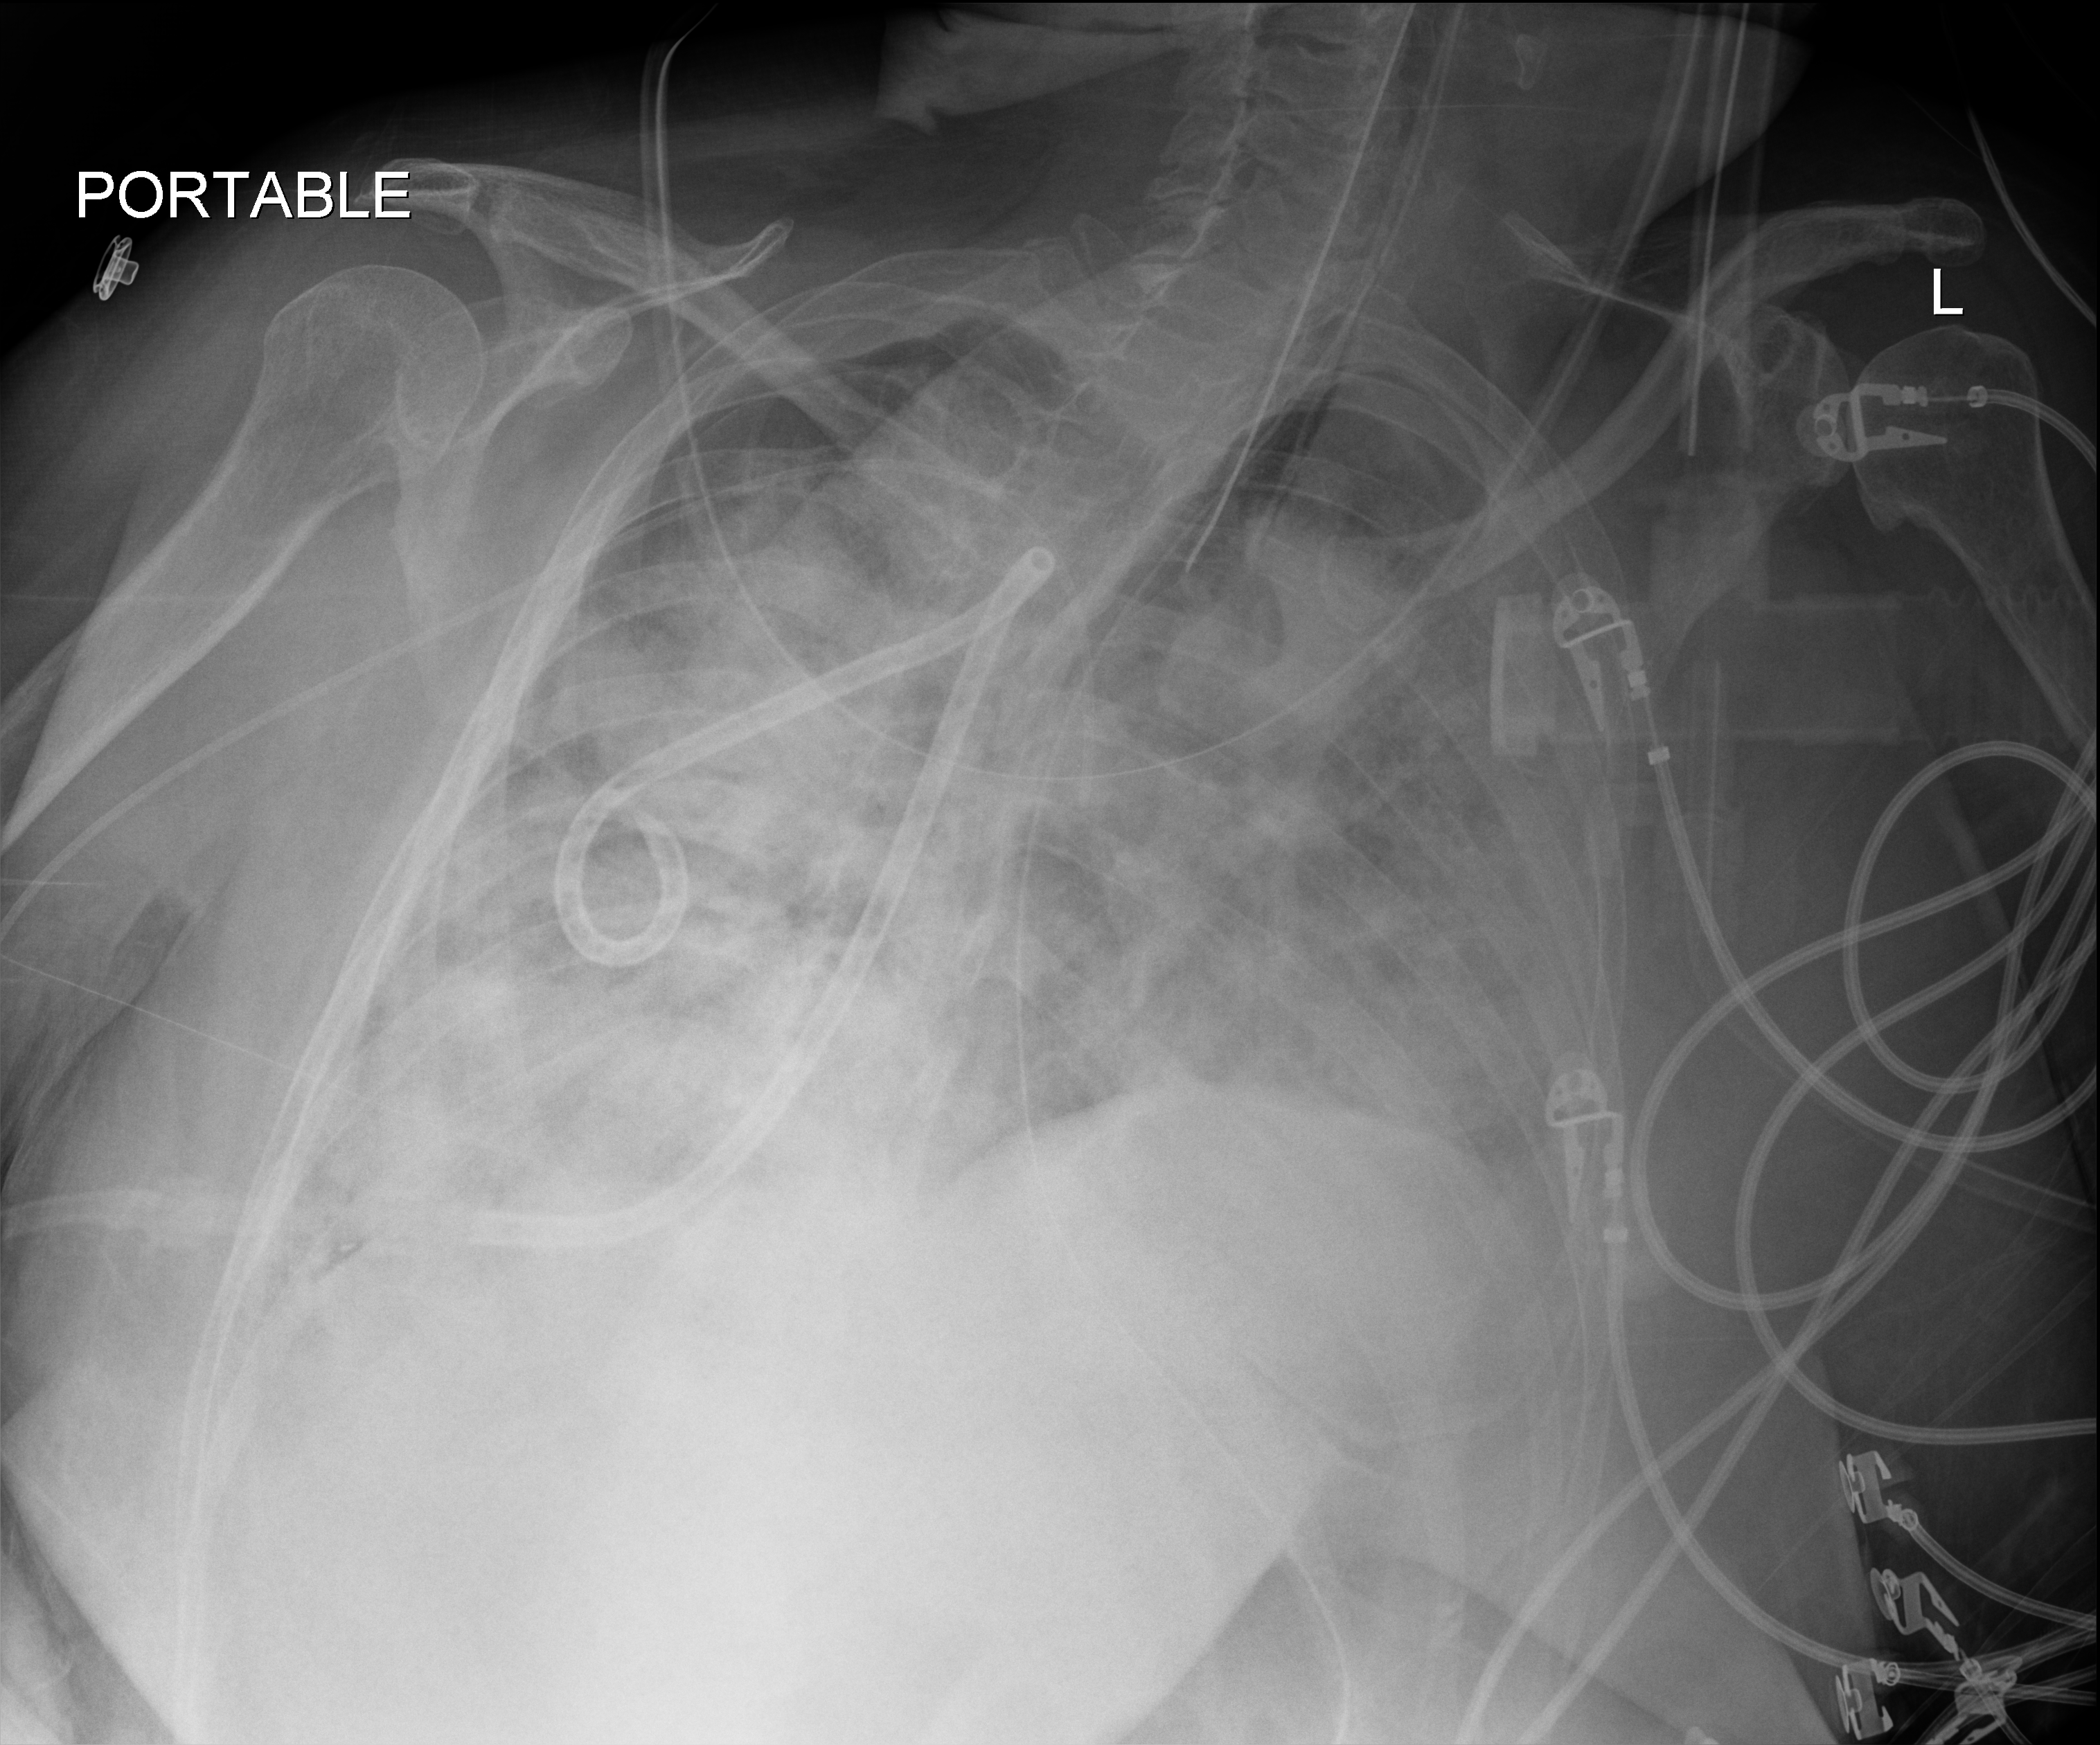
Chest radiograph, anteroposterior (AP) projection. Adult patient hospitalised with COVID-19, age 18–59 years.
Admission-level facts for this patient (not findings on this image; timing relative to this image not recorded):
- mechanically ventilated during this hospital stay: yes
- length of hospital stay: 15 days